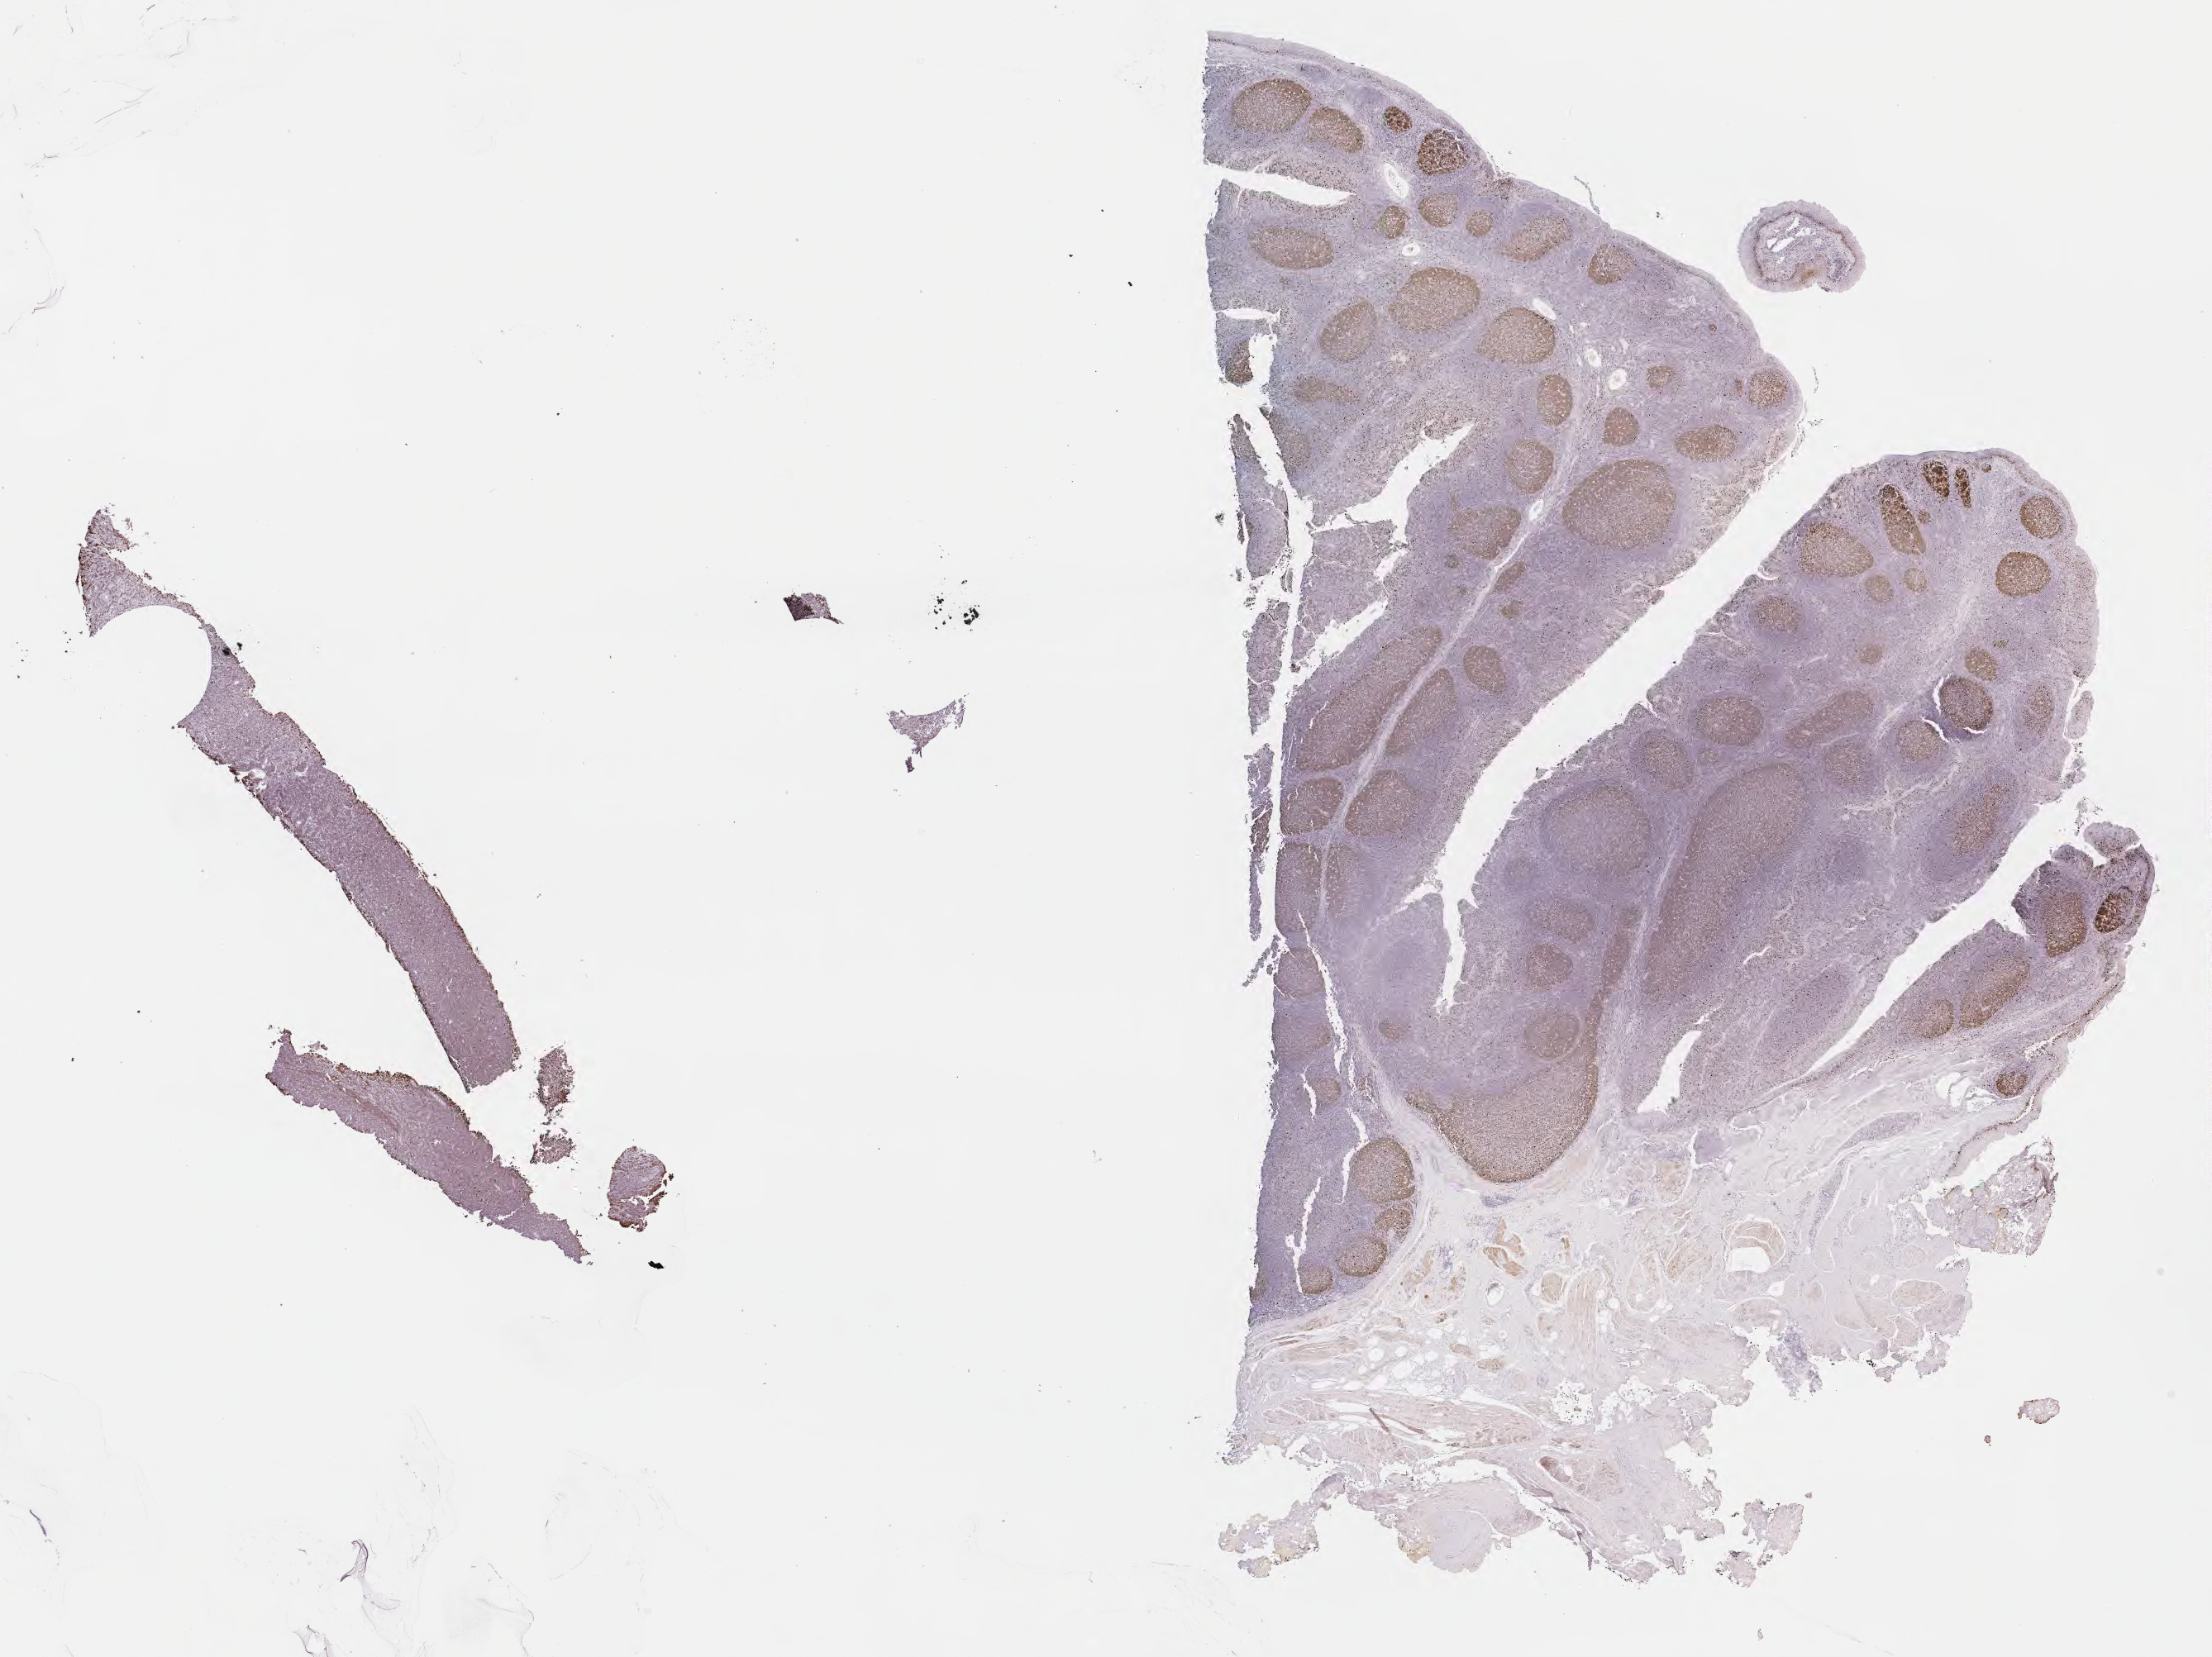
IHC for Ki-67, whole-slide image — shown as a low-resolution overview of the whole scanned area (about 21.6 x 16.2 mm). Specimen: tumor tissue. Anatomic site: liver. Patient: male, age 15 years.
Diagnosis: Burkitt lymphoma, NOS.